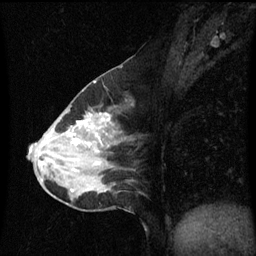
Breast MRI (dynamic contrast-enhanced), one sagittal slice. Position 31 of 60 along the scan axis. Dynamic contrast-enhanced series, image 2 of 3 at this slice position (ordered by acquisition). 1.5 T. TE 4.2 ms, TR 8.9 ms. 256 × 256 image matrix. Female patient, age 50 years. From the clinical record (not read from this slice): setting: breast cancer imaged before/during neoadjuvant chemotherapy; receptor status: HR-positive, HER2-negative.
Annotated regions visible in this slice (semi-automatic segmentation, software-assisted and operator-edited):
- analysis volume of interest (the breast-tissue region the enhancement analysis was run in; not a lesion): bounding box <33,90,136,209> (left, top, right, bottom; pixels)
- tumour enhancement mask (voxels above the 70 % enhancement threshold inside the analysis volume of interest): <53,114,111,145>